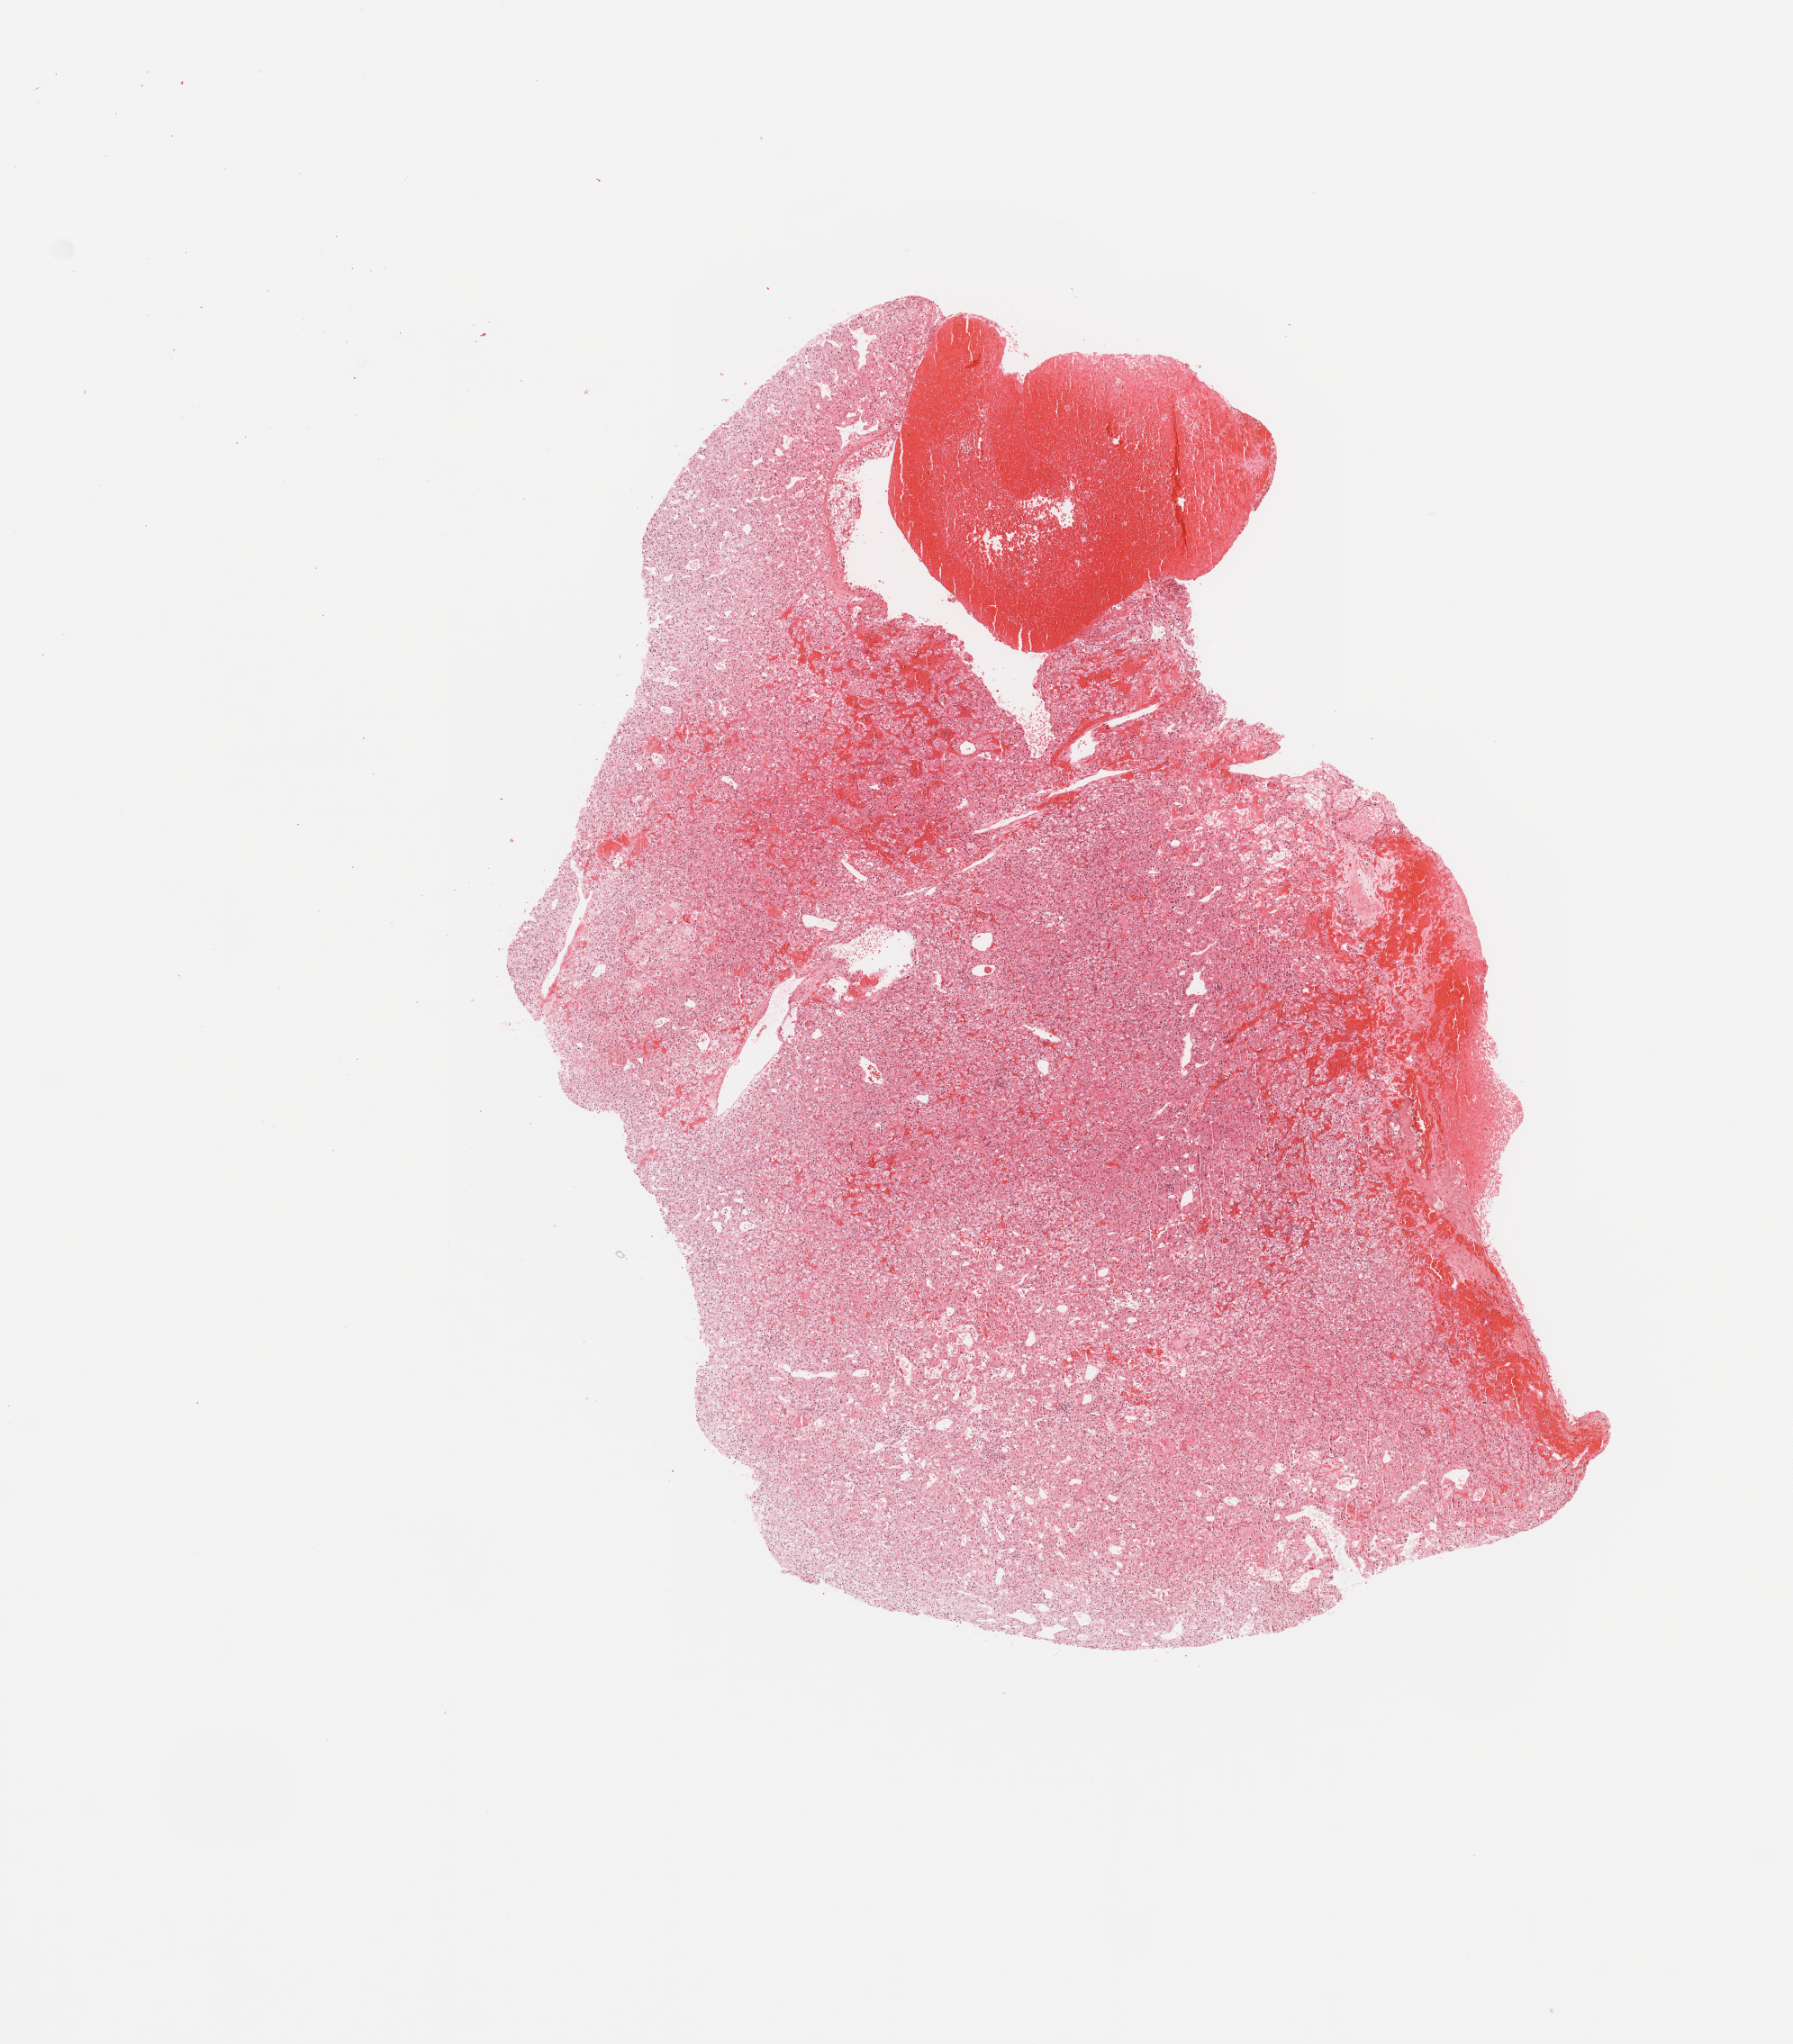
Digitized Hematoxylin and eosin (H&E) stained tissue section (whole slide) — whole scanned area (about 7.9 x 9.0 mm, slide scanned at 20x) shown as a low-resolution overview, tumour tissue sample, sampled site: kidney. Patient: male, age 83 years. Histologic grade: G2 (moderately differentiated). Pathologist review of this section (percent, as recorded): tumour nuclei 90%, necrosis 5%.
• diagnosis: Renal cell carcinoma, NOS
• AJCC pathologic stage: I
• primary tumour site (as recorded): middle